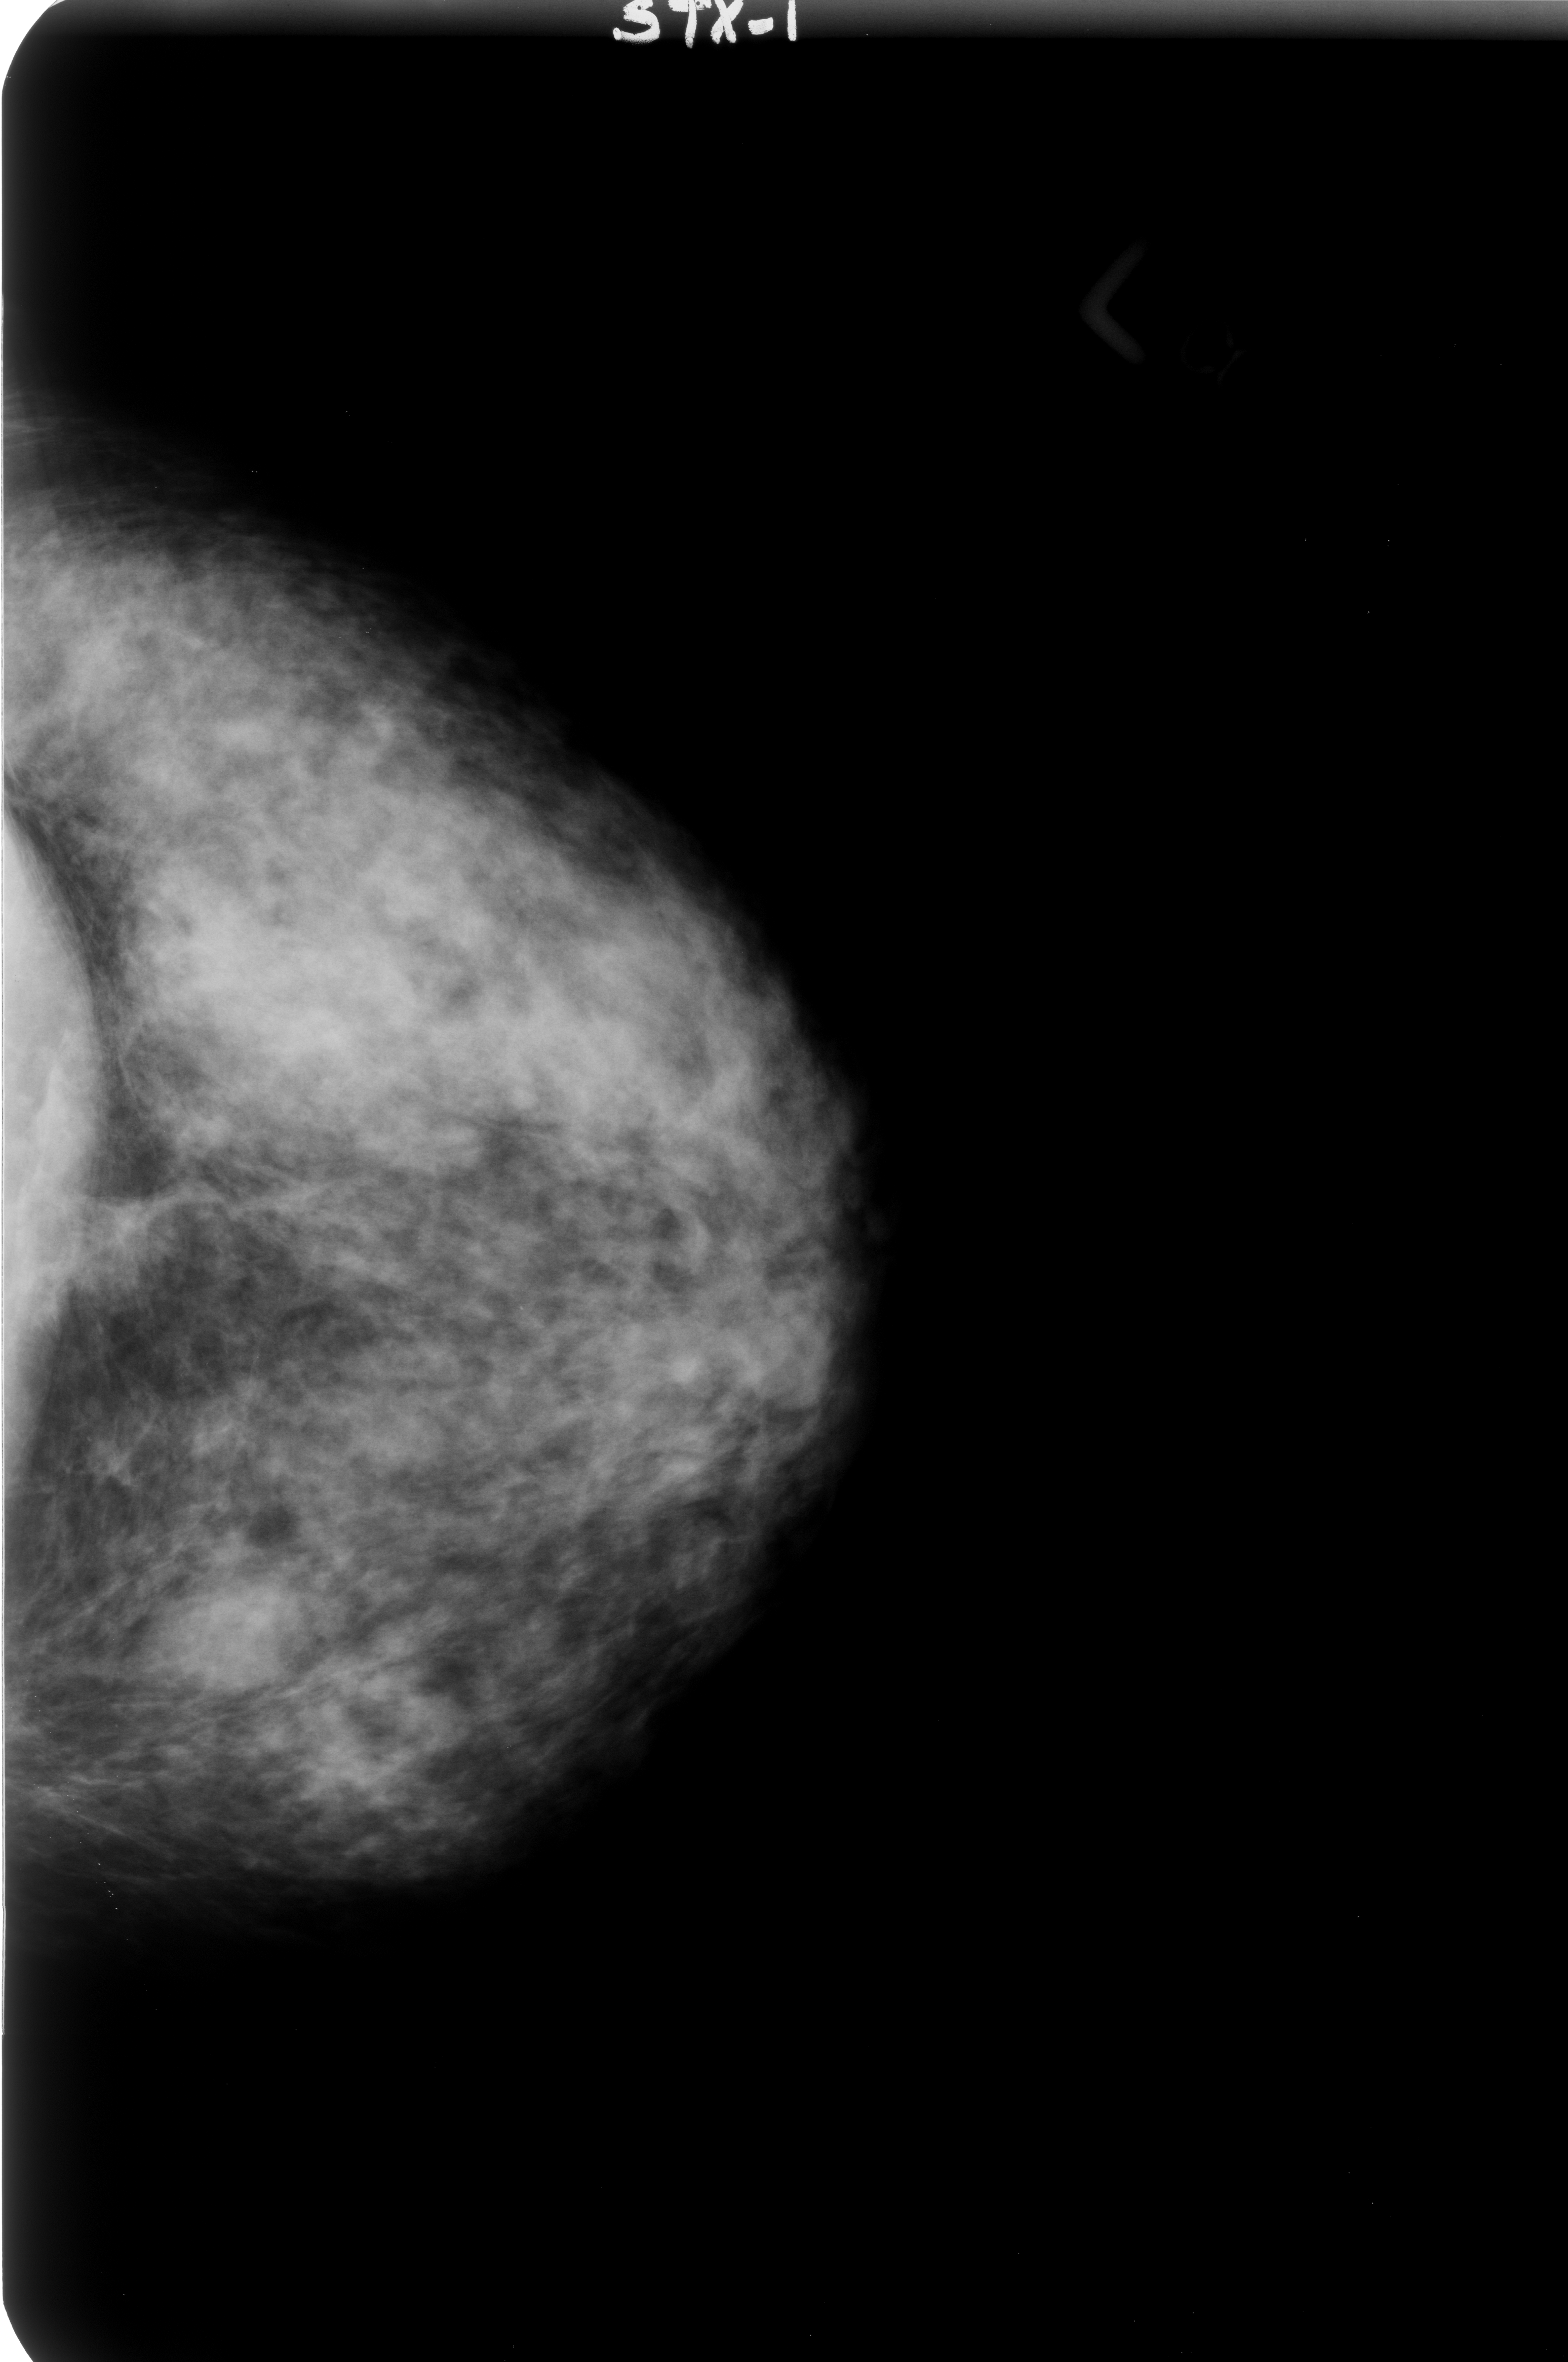
Scanned film-screen mammogram; left breast; CC view; breast composition: heterogeneously dense (BI-RADS density category 3 of 4).
- Marked abnormality: mass, shape lobulated, margins circumscribed; BI-RADS assessment category 3; pathology (as recorded): benign.